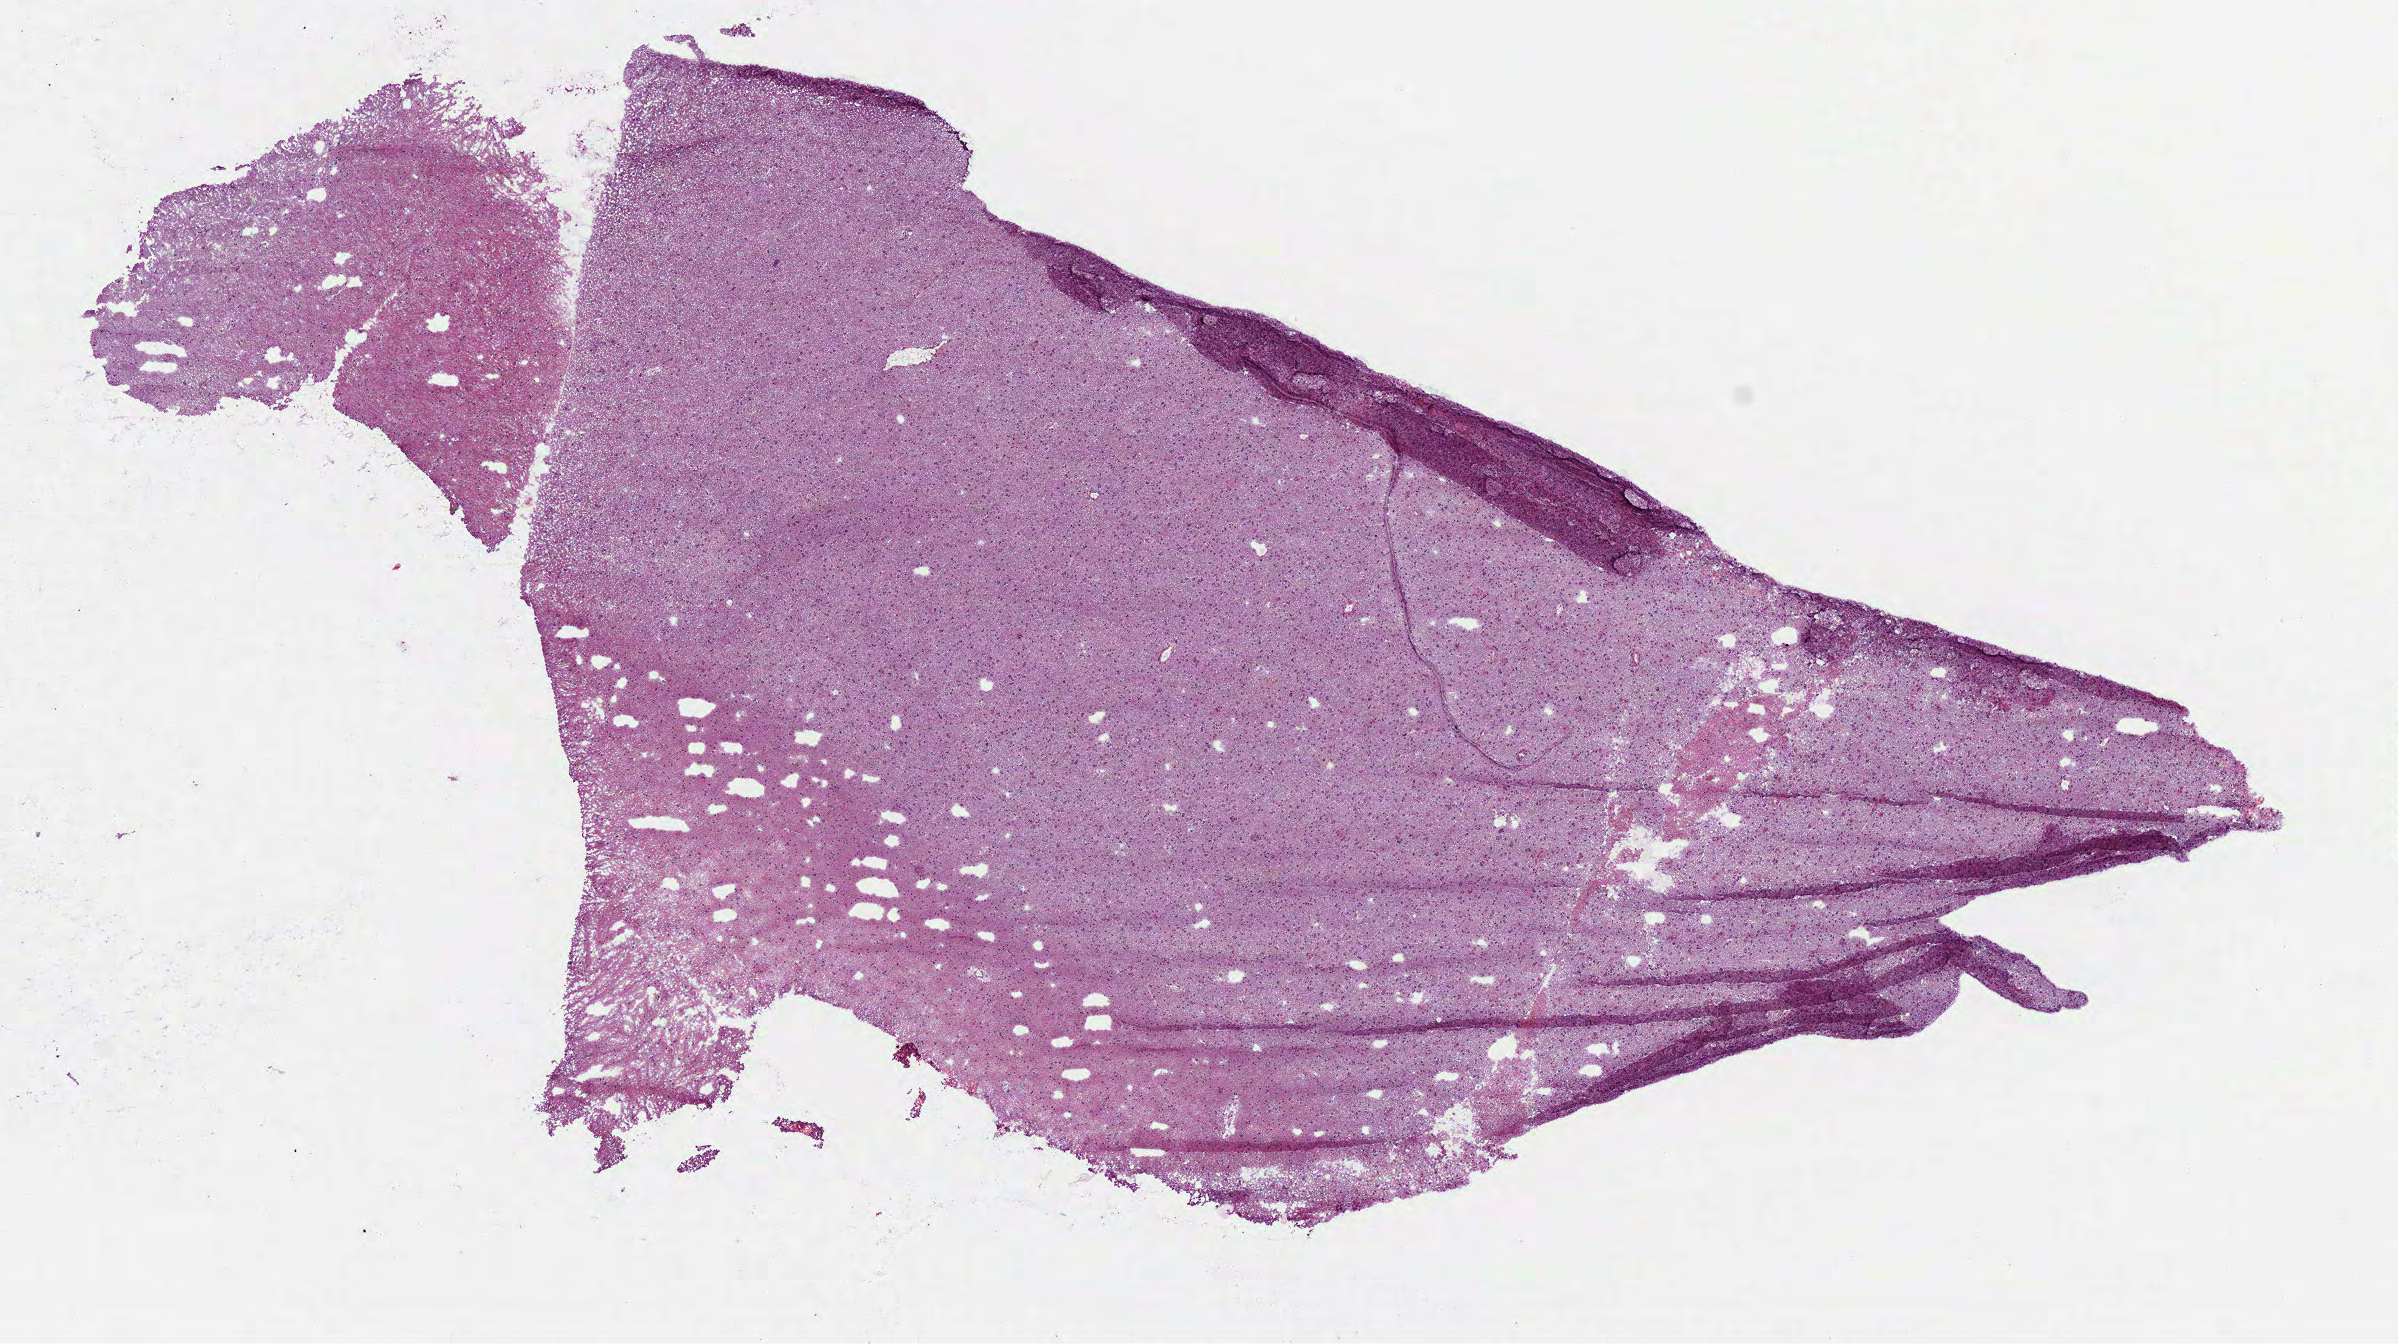
Whole-slide histology image, H&E-stained — whole scanned area (about 9.7 x 5.4 mm) shown as a low-resolution overview; frozen section from the top of the tissue portion; brain, primary tumour sample. Male patient; age at initial diagnosis 69 years. Histologic grade: G3 (poorly differentiated). Slide review estimates, as recorded: tumour cells 100%, tumour nuclei 60%, normal cells 0%, stromal cells 0%, necrosis 0%.
Diagnosis: Astrocytoma, anaplastic (cerebrum).